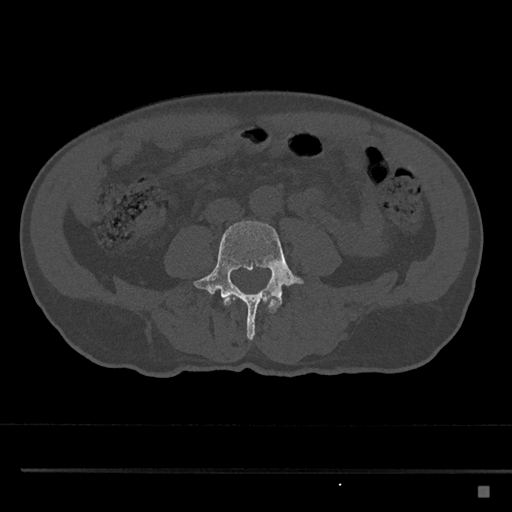
CT including the spine, one axial slice. Position 641 of 797 along the scan axis. 120 kVp. Bone window (W 1800 / L 400 HU). 512 × 512 image matrix. Male patient, age 59 years. From the clinical record (not read from this slice): primary cancer: prostate.
Annotated regions visible in this slice (semi-automatically segmented with operator editing):
- L3 vertebra: bounding box [x1, y1, x2, y2] px = [224, 296, 279, 313]
- L4 vertebra: [193, 221, 304, 340]
- L5 vertebra: [207, 290, 209, 292]